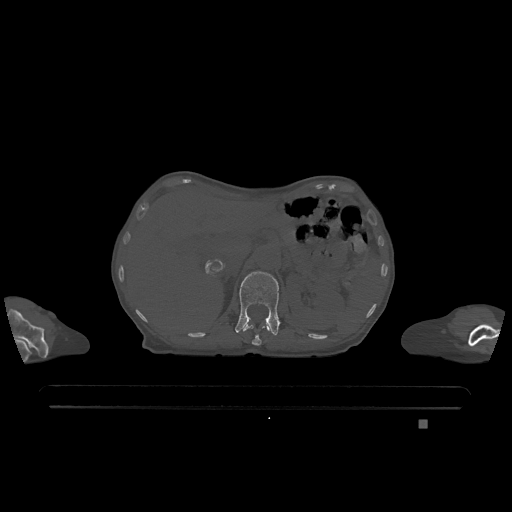
CT including the spine, one axial slice; position 490 of 1317 along the scan axis; bone window (W 1800 / L 400 HU); 0.5 mm slice thickness; 512 × 512 image matrix, field of view 500 × 500 mm. Female patient, age 74 years. Case-level facts recorded for this patient, not image findings: primary cancer: lung; vertebrae with lytic lesions (as recorded): T1, T4, T5, T6, L4, L5.
Annotated regions visible in this slice (semi-automatically segmented with operator editing):
- L1 vertebra: box from (x=235, y=271) to (x=280, y=336) px
- T12 vertebra: (x=243, y=324)–(x=270, y=346)